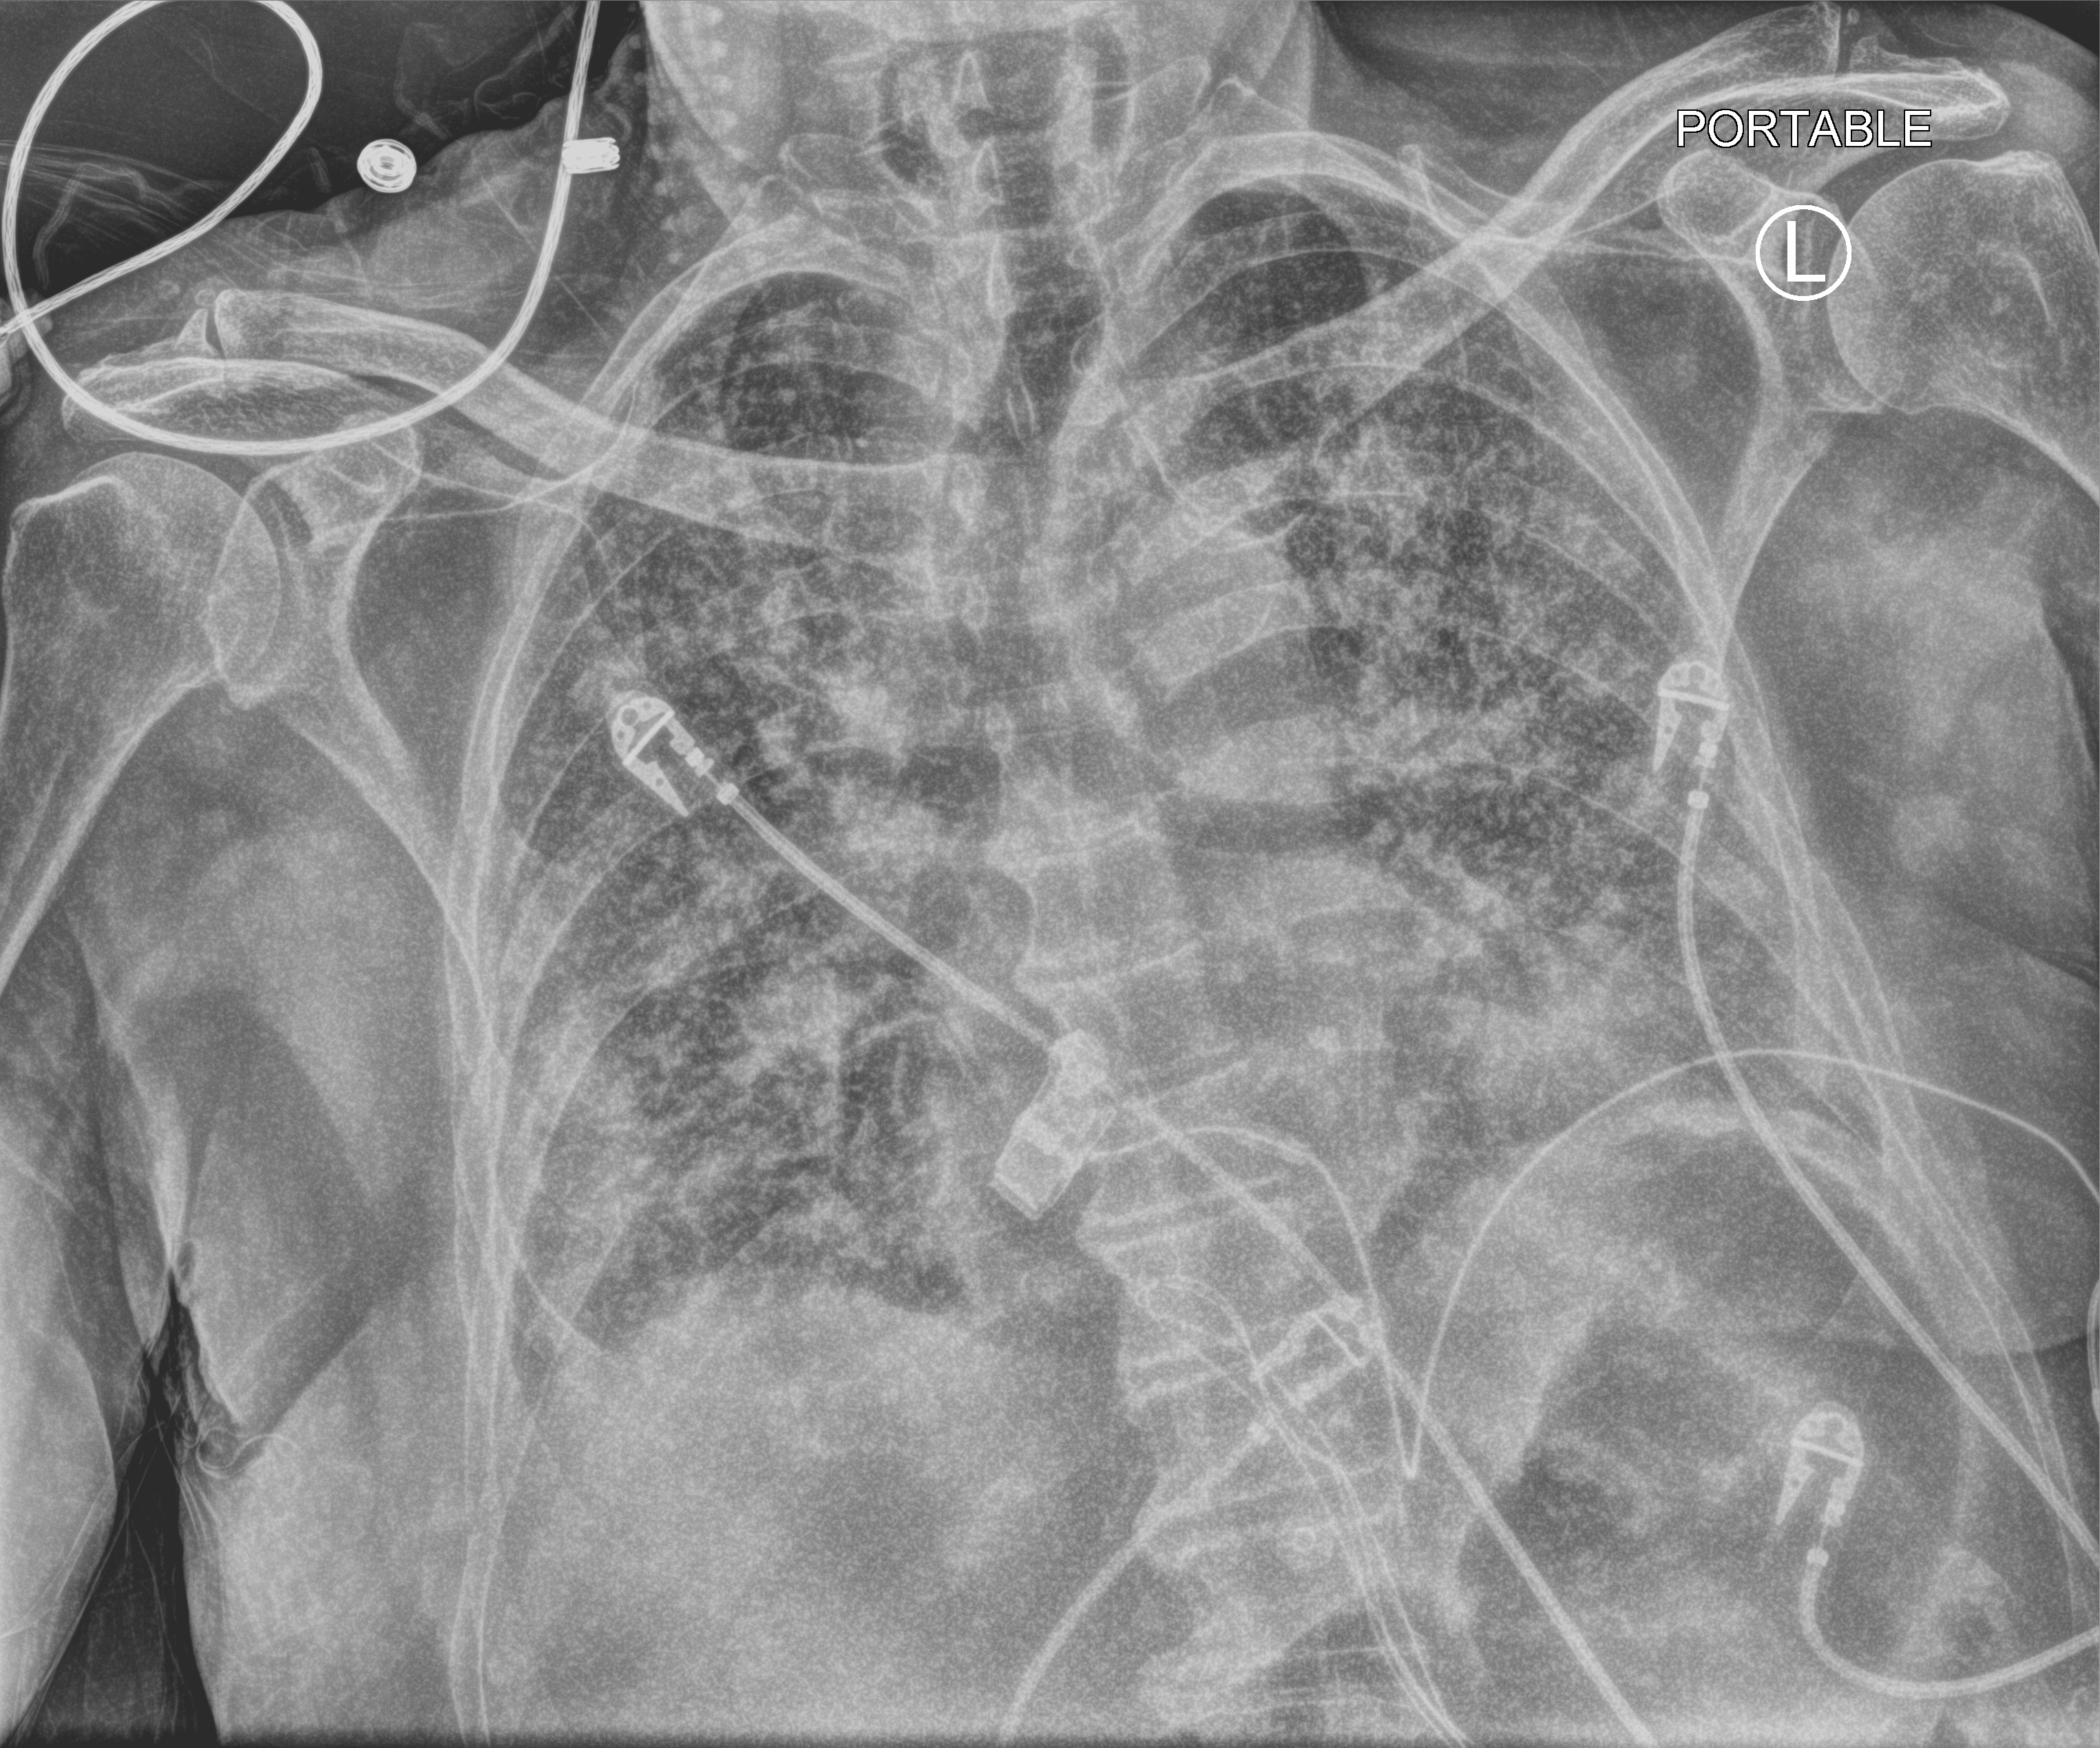
Chest X-ray (portable), anteroposterior (AP) projection. Patient hospitalised with COVID-19; male, aged 75–90 years.
Hospital-stay facts (about this admission, not read from this image; timing relative to this image not recorded): admitted to intensive care during this hospital stay: yes; mechanically ventilated during this hospital stay: yes.